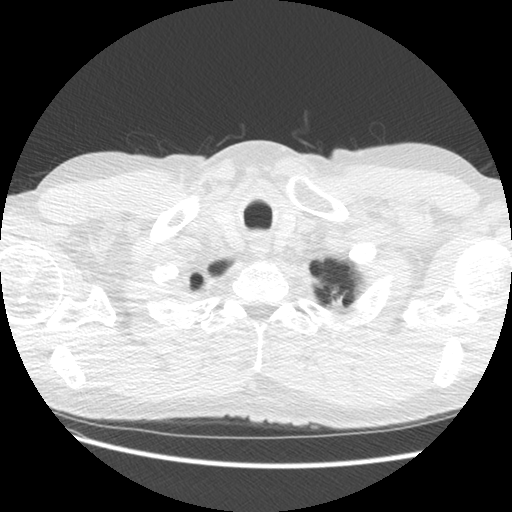
Low-dose screening chest CT, axial slice; second annual screen; lung window (W 1500 / L -600 HU); 2.5 mm slice thickness; standard (soft-tissue) reconstruction kernel (STANDARD). Male, age 63 years at enrolment.
Lesion marked by an expert reader, bounding box [x1, y1, x2, y2] px = [319, 278, 359, 315]. The screening reader recorded 2 non-calcified nodules or masses ≥4 mm on this exam (left upper lobe, right lower lobe); which of them this box marks is not recorded. Official screen result: positive, other. Lung cancer was diagnosed 104 days after this screen: adenocarcinoma, NOS, left upper lobe, moderately differentiated (G2), stage IB (AJCC 6th edition), 14 mm at pathology.